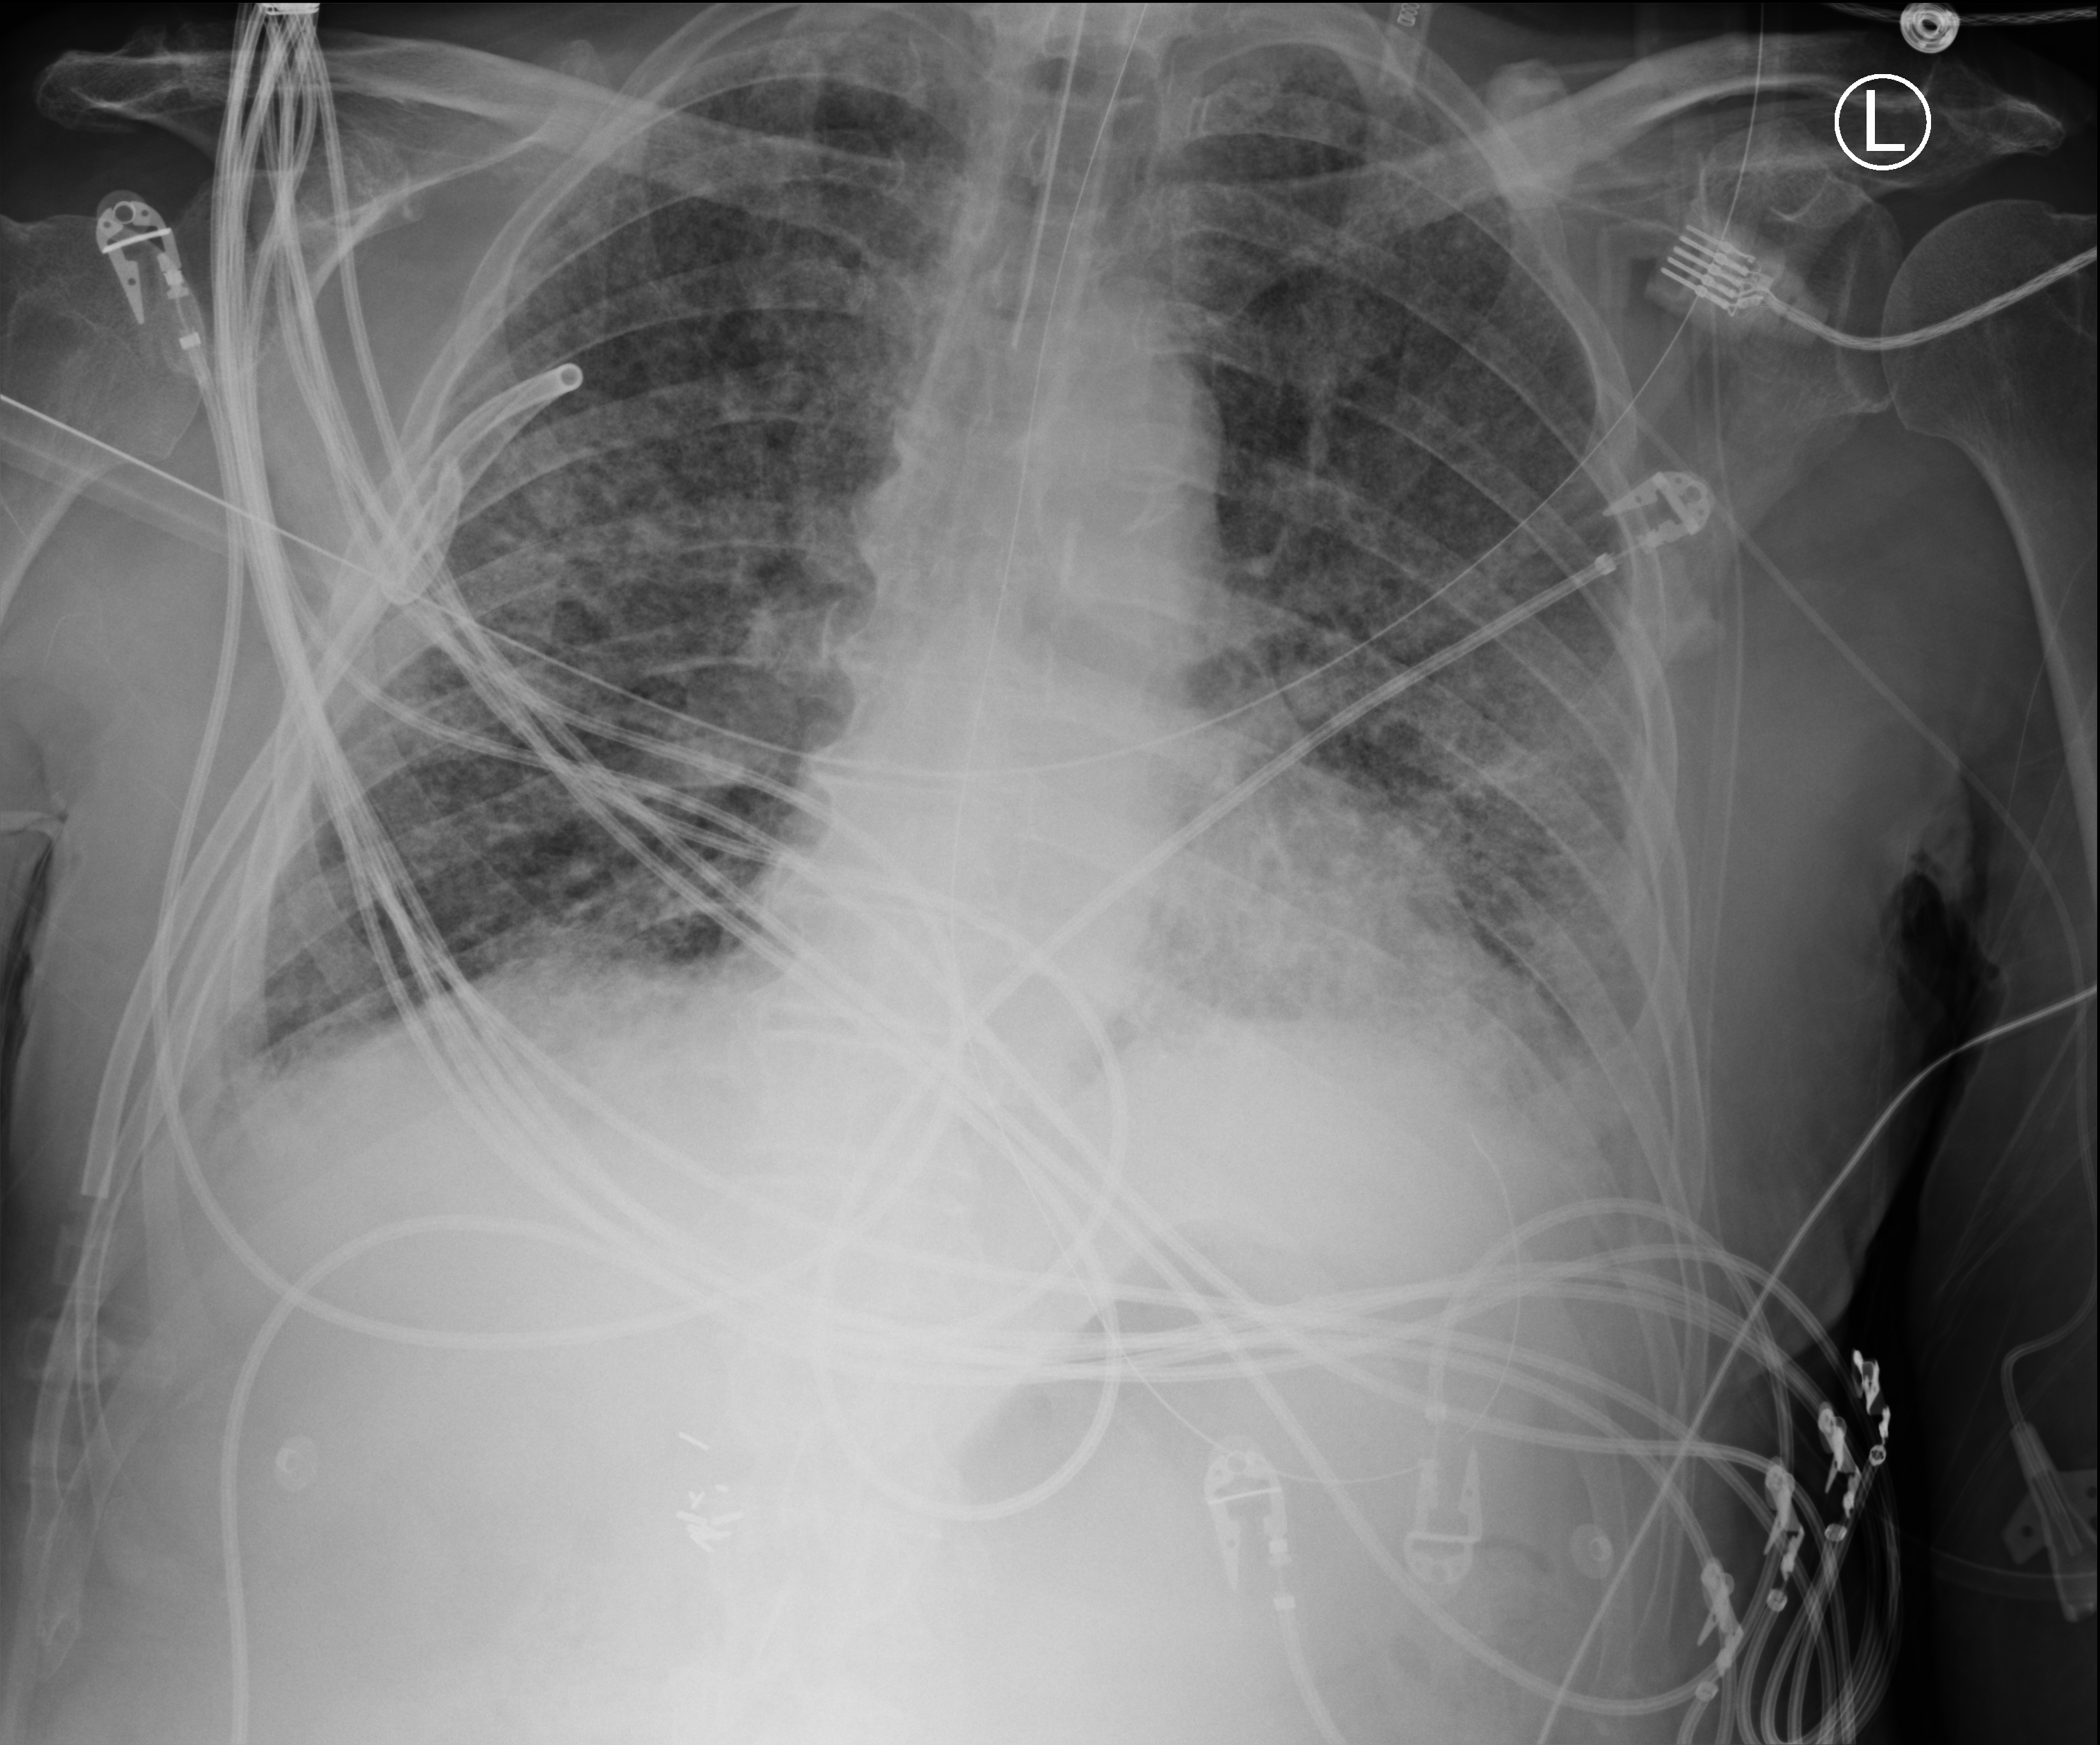
Portable chest radiograph, anteroposterior (AP) projection. Patient hospitalised with COVID-19; male, aged 75–90 years.
From the hospital-stay record, not from the radiograph (when in the stay this image was taken is not recorded): other chronic lung disease (admission record): no; mechanically ventilated during this hospital stay: yes; admitted to intensive care during this hospital stay: yes.